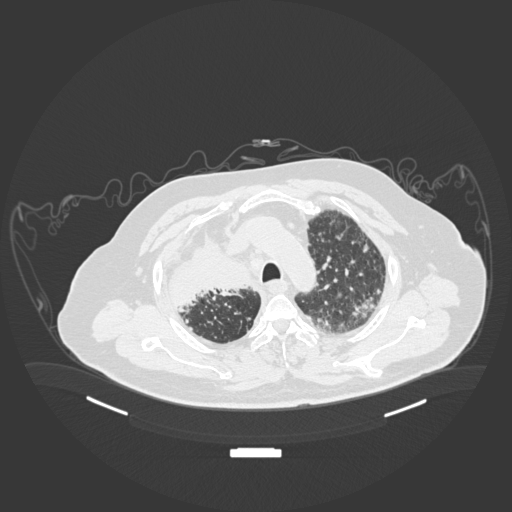
Chest CT, one axial slice. Slice 146 of 201 in the series (ordered by position). Reconstruction kernel B30f. 120 kVp. Lung window (W 1500 / L -600 HU). 1 mm slice thickness. 512 × 512 image matrix, field of view 500 × 500 mm. Patient: male, 69 years. From the clinical record (not read from this slice): clinical TNM (as recorded): T4 N3 M1.
Structures marked on this image (bounding box drawn by a radiologist):
- lung tumour (recorded histology: adenocarcinoma): bounding box (x1, y1, x2, y2) in pixels: (165, 229, 254, 309)